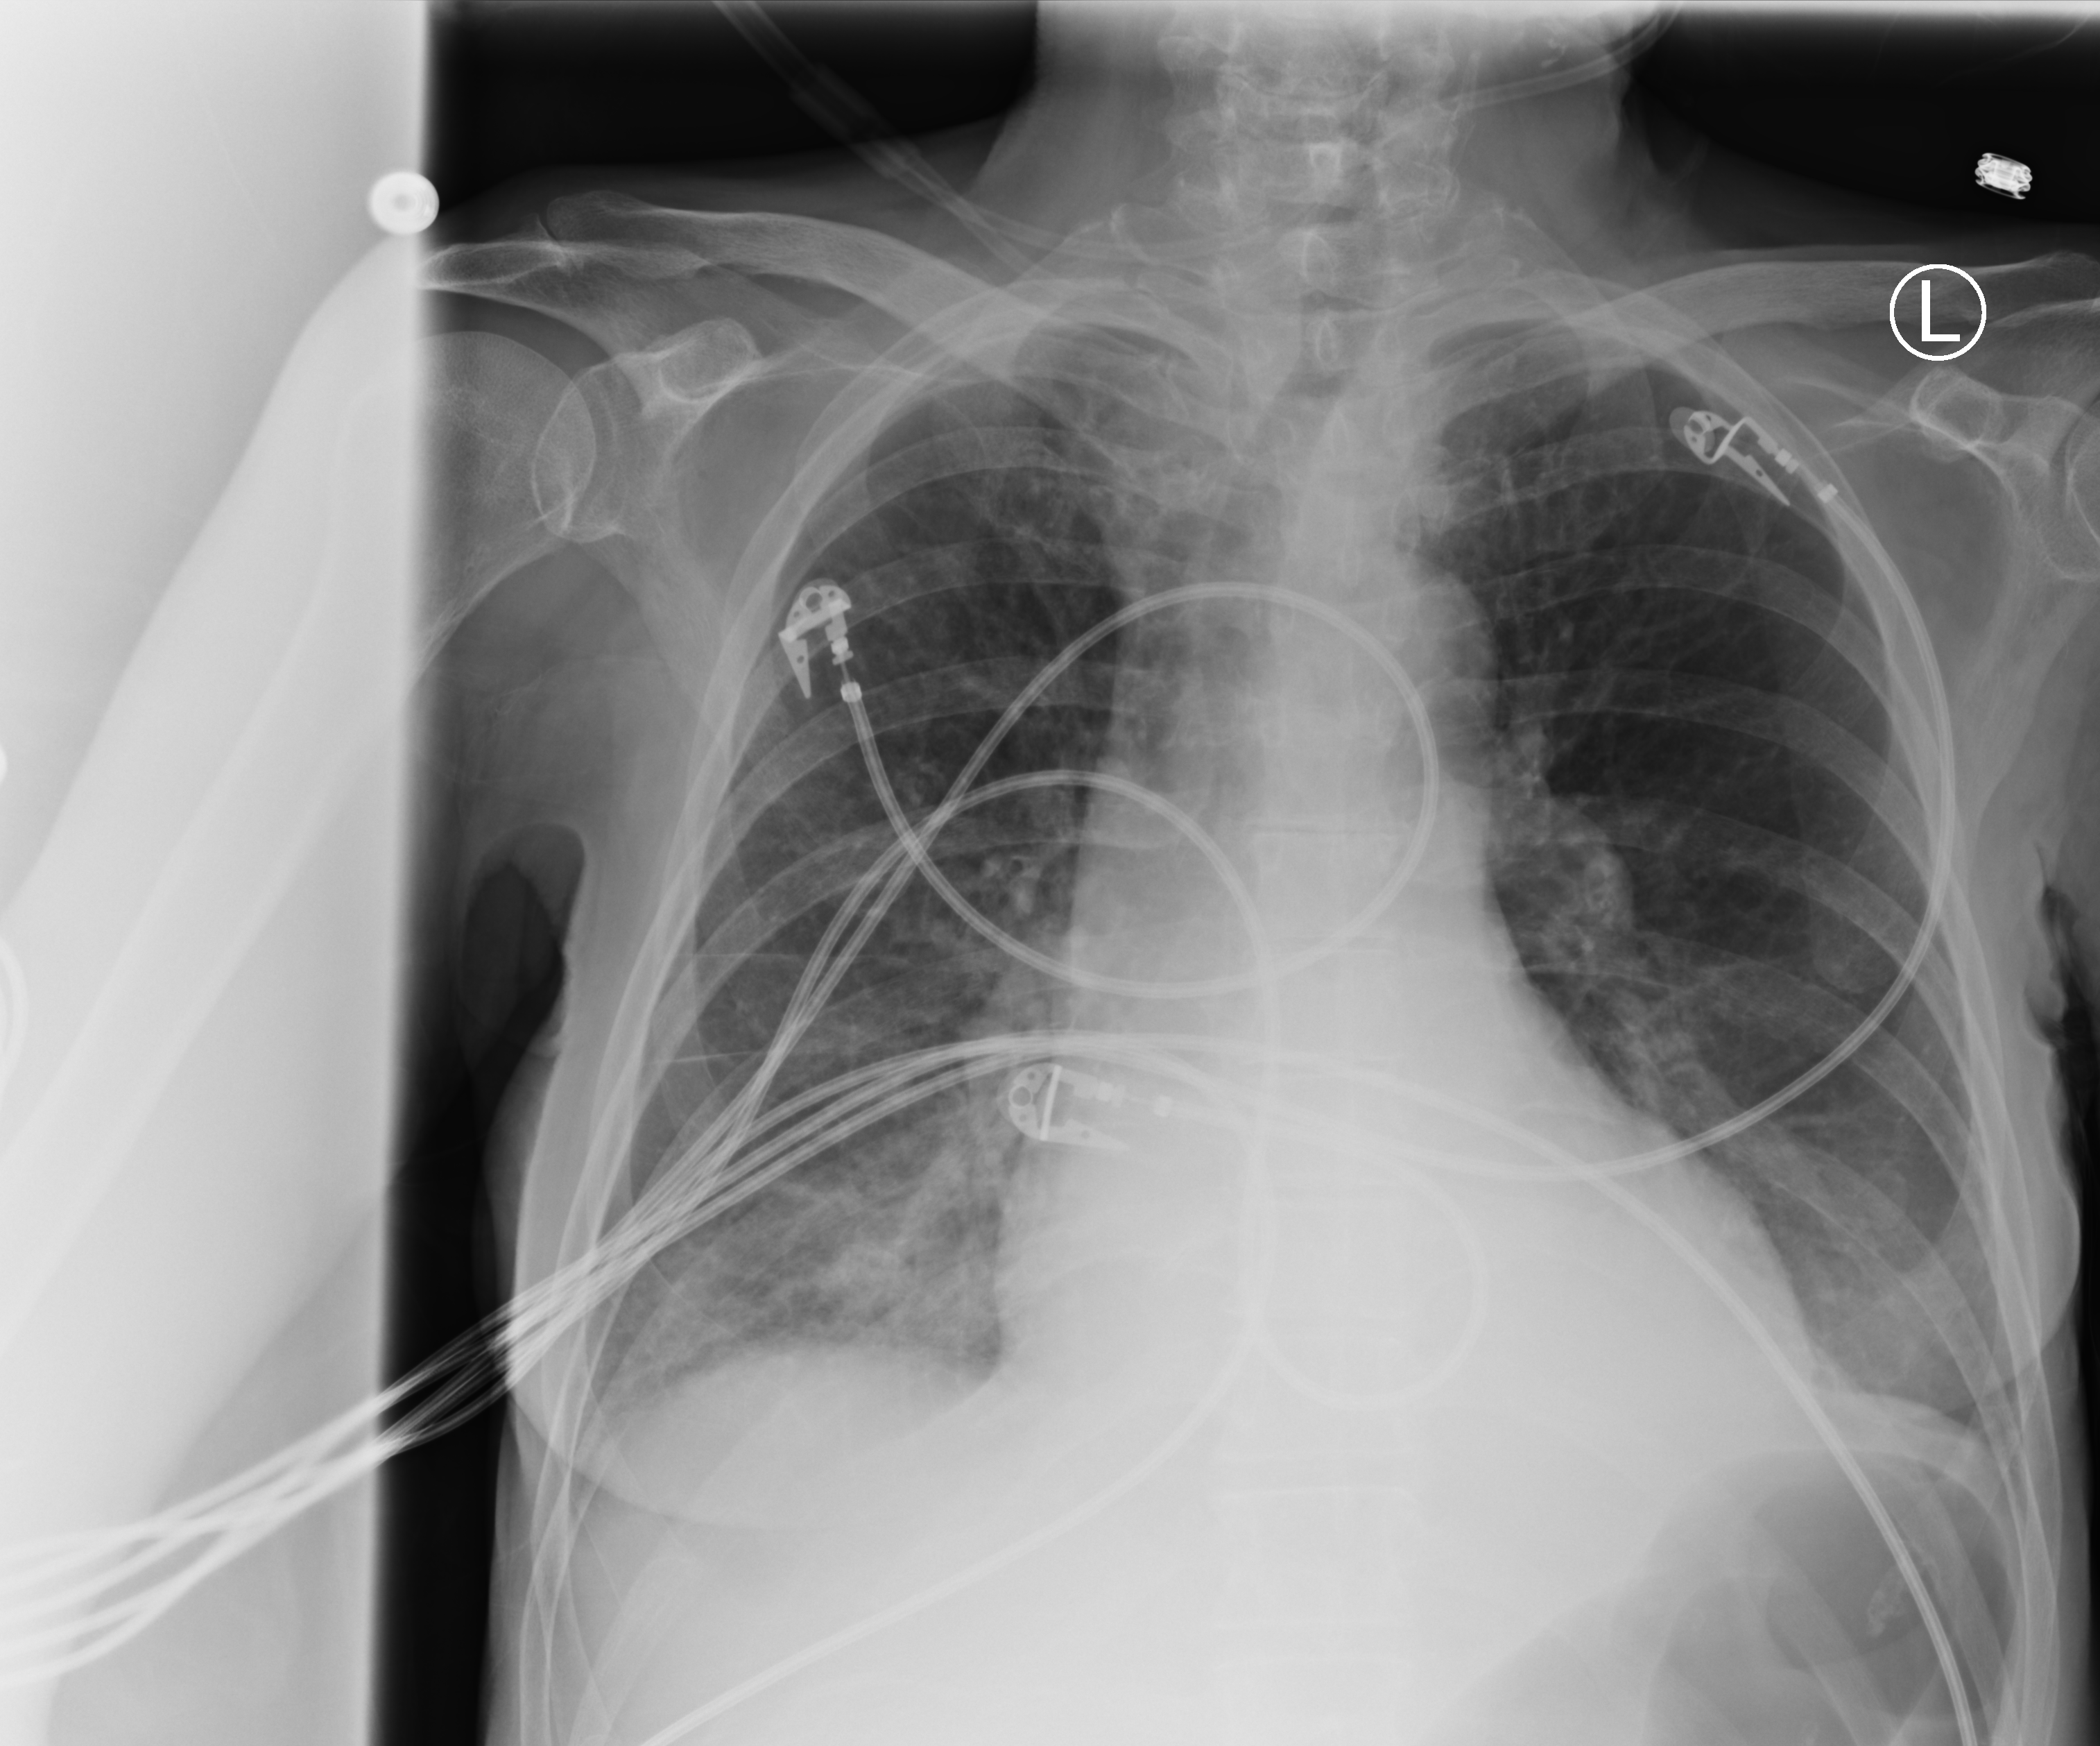
Portable chest radiograph, anteroposterior (AP) projection. Patient hospitalised with COVID-19; female, aged 60–74 years.
From the hospital-stay record, not from the radiograph (when in the stay this image was taken is not recorded): length of hospital stay: 38 days; mechanically ventilated during this hospital stay: yes.